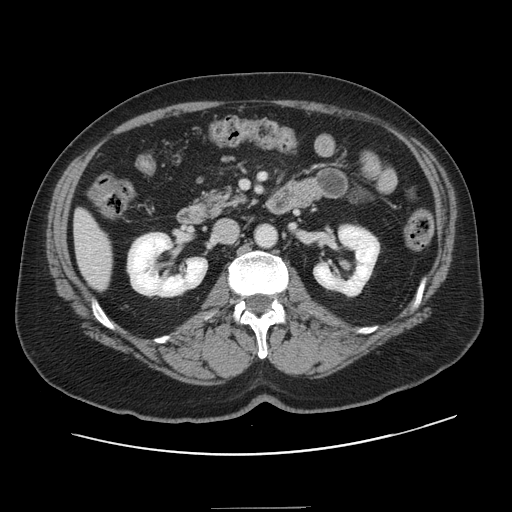
Contrast-enhanced abdominal CT, one axial slice; slice 52 of 143 in the series (ordered by position); 120 kVp; intravenous contrast given; soft-tissue window (W 400 / L 40 HU); 2.5 mm slice thickness; 512 × 512 image matrix, field of view 402 × 402 mm. Male patient, age 62 years. Case-level facts recorded for this patient, not image findings: diagnosis: colorectal cancer liver metastases, imaged before liver resection; multiple liver metastases: yes; largest metastasis: 2.7 cm.
Structures marked on this image (manually delineated by an expert):
- liver: bounding box <75,213,112,289> (left, top, right, bottom; pixels)